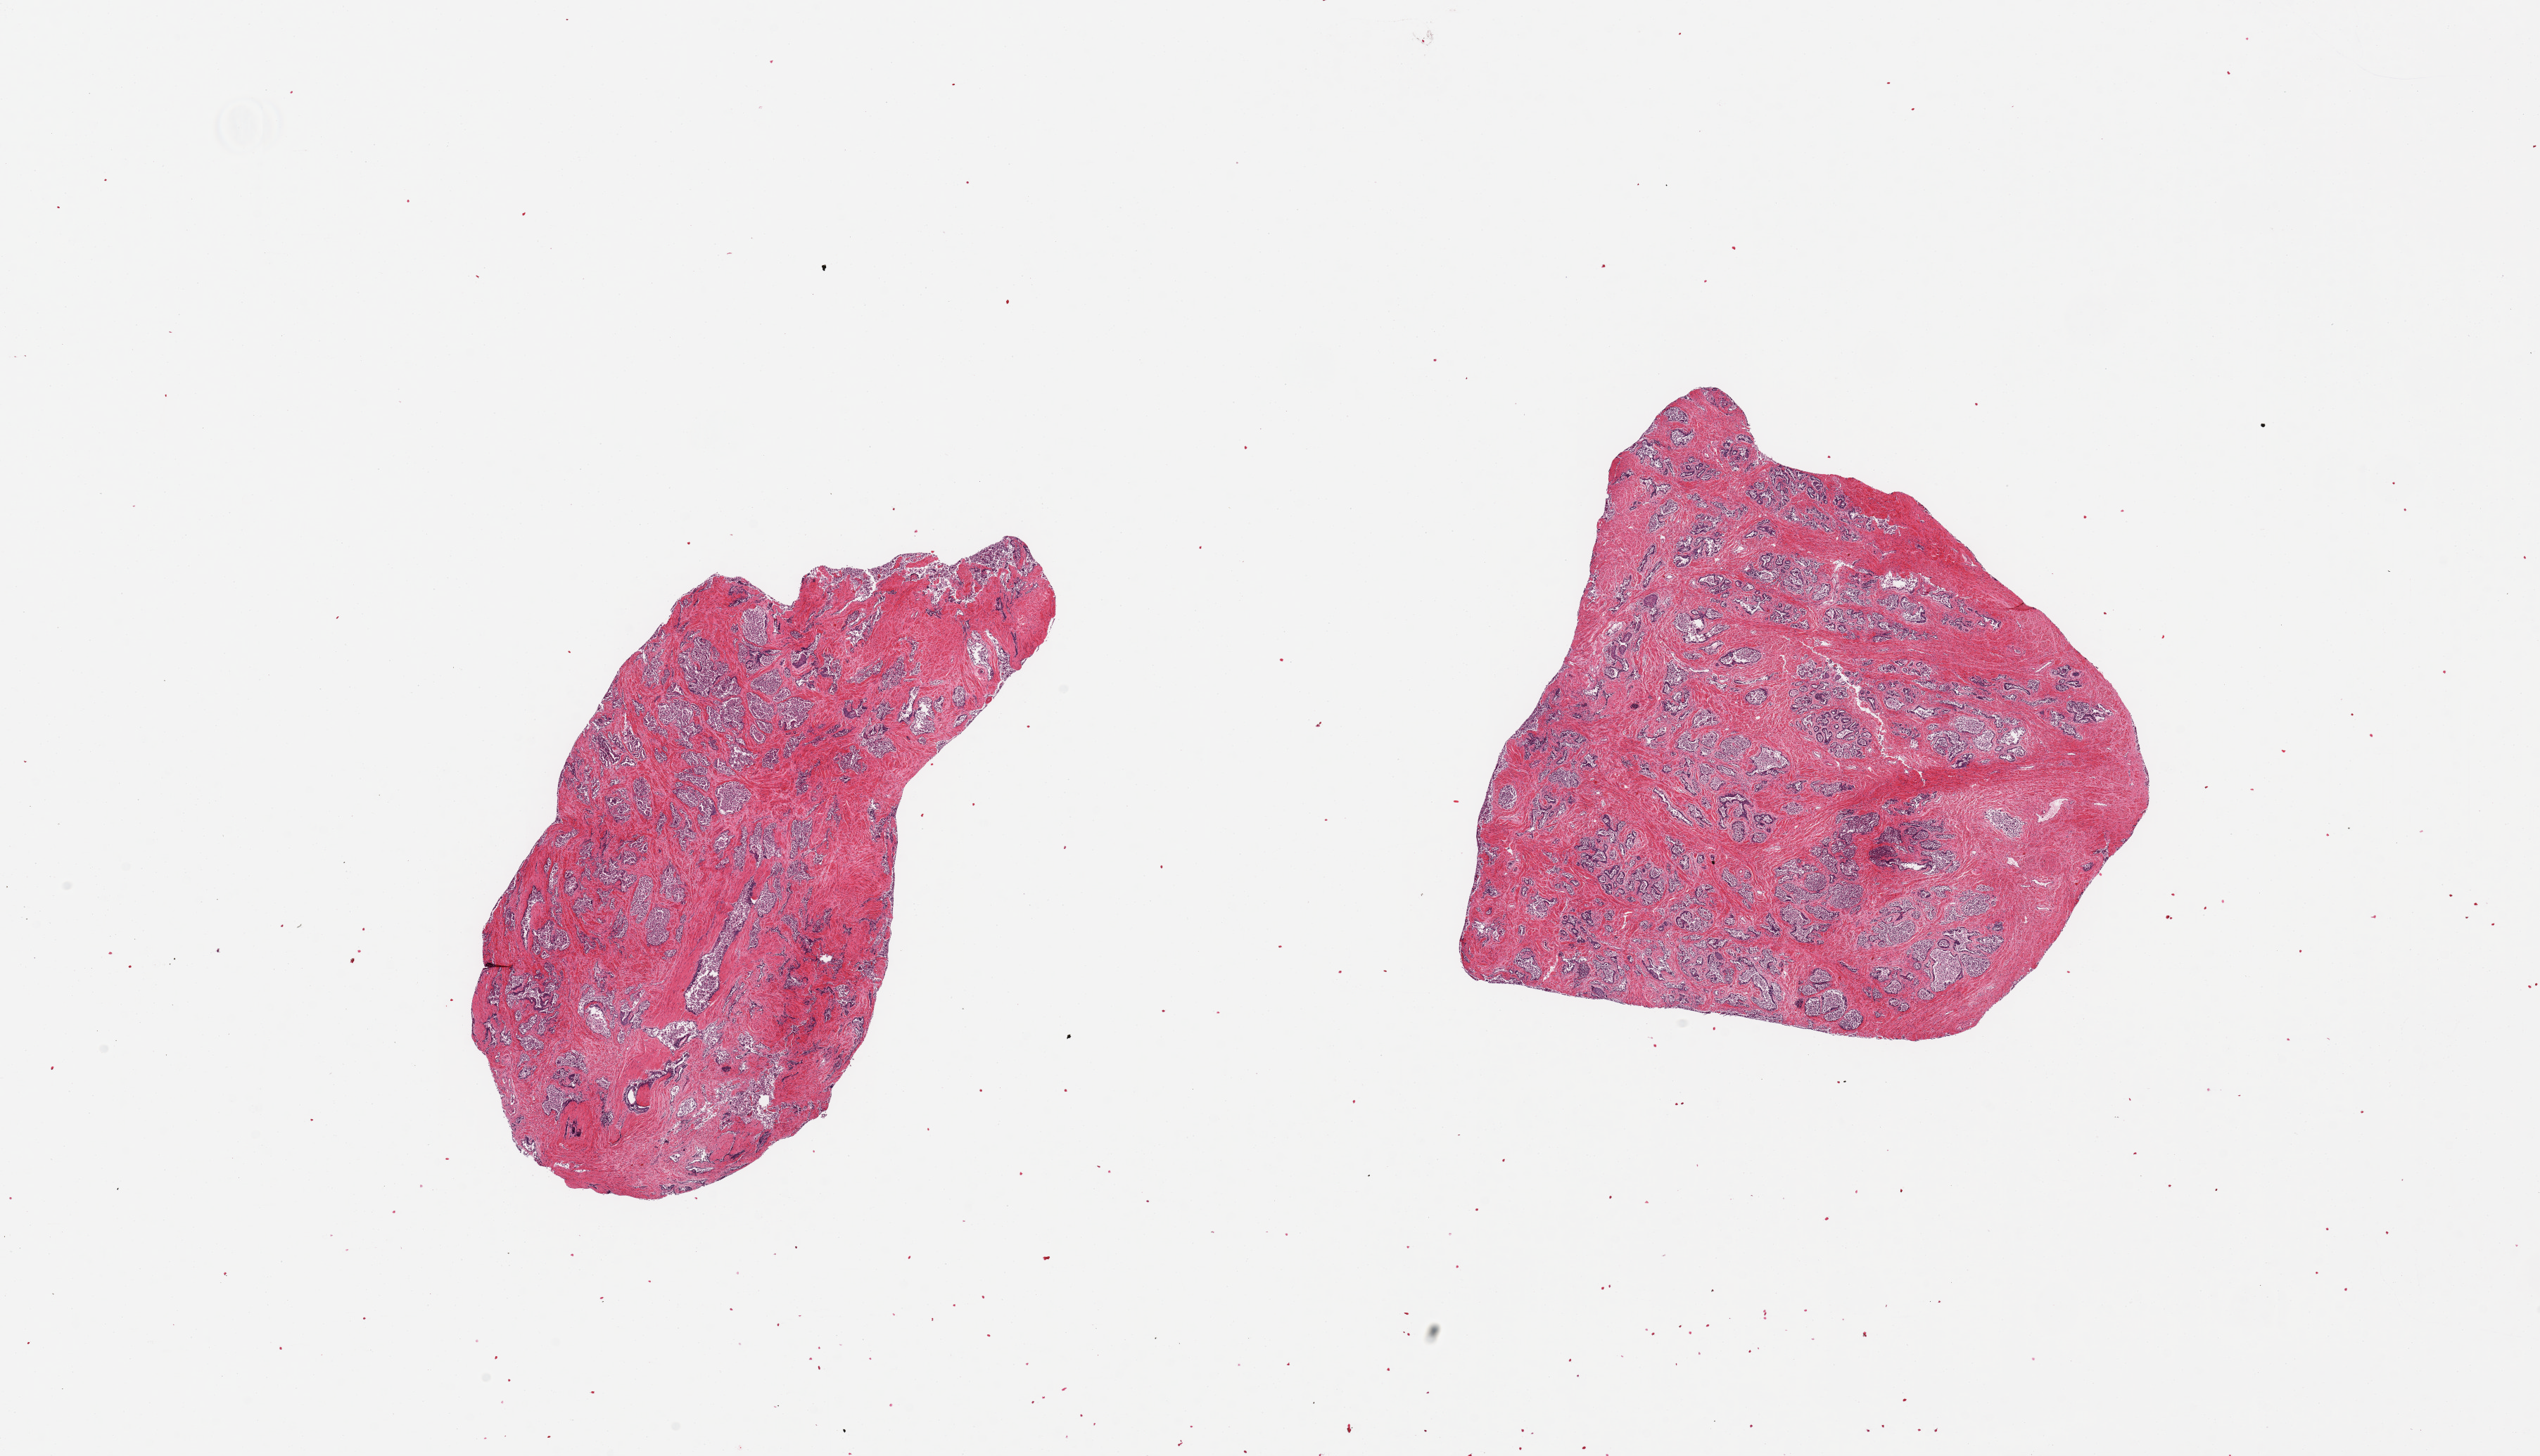
H&E whole-slide image — whole scanned area (about 28.5 x 16.4 mm) shown as a low-resolution overview; PAXgene-fixed, paraffin-embedded tissue; sampled site (target tissue): prostate; donor tissue sample. Male donor.
Review note (as recorded): 2 pieces; fibromuscular stroma and glands with predominantly sloughed epithelium.